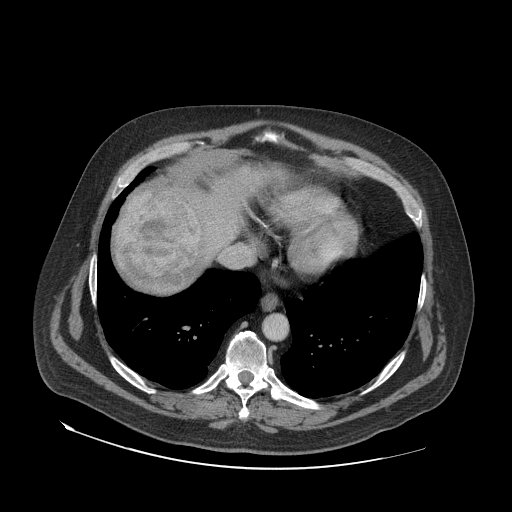
Contrast-enhanced abdominal CT (liver protocol), one axial slice; position 68 of 79 along the scan axis; 140 kVp; soft-tissue window (W 400 / L 40 HU); 512 × 512 image matrix. From the clinical record (not read from this slice): diagnosis: hepatocellular carcinoma (patient treated with transarterial chemoembolisation; whether this scan precedes or follows treatment is not stated here); TNM stage (as recorded): Stage-IVA; Child-Pugh class: A; tumour nodularity: multinodular.
Annotated regions visible in this slice (semi-automatically segmented with operator editing):
- abdominal aorta: box from (x=264, y=315) to (x=286, y=338) px
- liver parenchyma outside the tumour (the mass and vessels are separate outlines, so this box may not span the whole liver): (x=116, y=166)–(x=284, y=292)
- mass: (x=118, y=187)–(x=202, y=285)